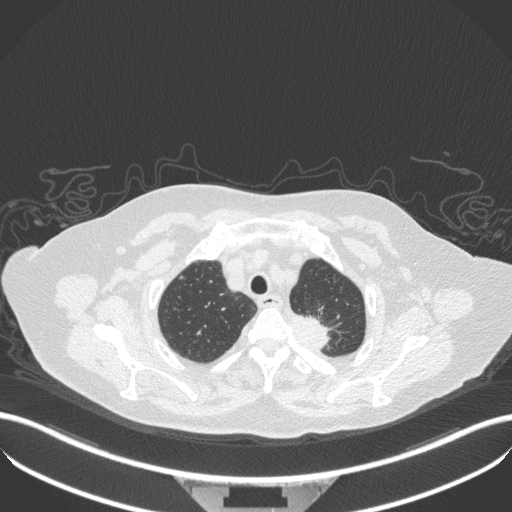
Chest CT, one axial slice. Position 293 of 353 along the scan axis. Reconstruction kernel B31f. Lung window (W 1500 / L -600 HU). 512 × 512 image matrix, field of view 400 × 400 mm. Female patient, age 81 years. Case-level facts recorded for this patient, not image findings: clinical TNM (as recorded): T2a N0 M0.
Annotated regions visible in this slice (rectangle marked by the reading radiologist):
- lung tumour (recorded histology: adenocarcinoma): box from (x=283, y=309) to (x=340, y=365) px